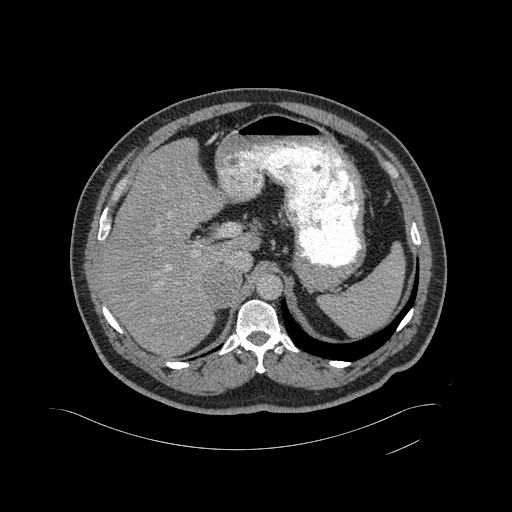
Contrast-enhanced abdominal CT, one axial slice; position 333 of 433 along the scan axis; 120 kVp; soft-tissue window (W 400 / L 40 HU); 2 mm slice thickness; 512 × 512 image matrix. Patient: male, 56 years. Case-level facts recorded for this patient, not image findings: diagnosis: adrenocortical carcinoma; tumour side: right adrenal; tumour size at pathology: 11.6 cm; Ki-67 index: 50 %.
Annotated regions visible in this slice (semi-automatically segmented with operator editing):
- mass: box from (x=205, y=267) to (x=239, y=307) px